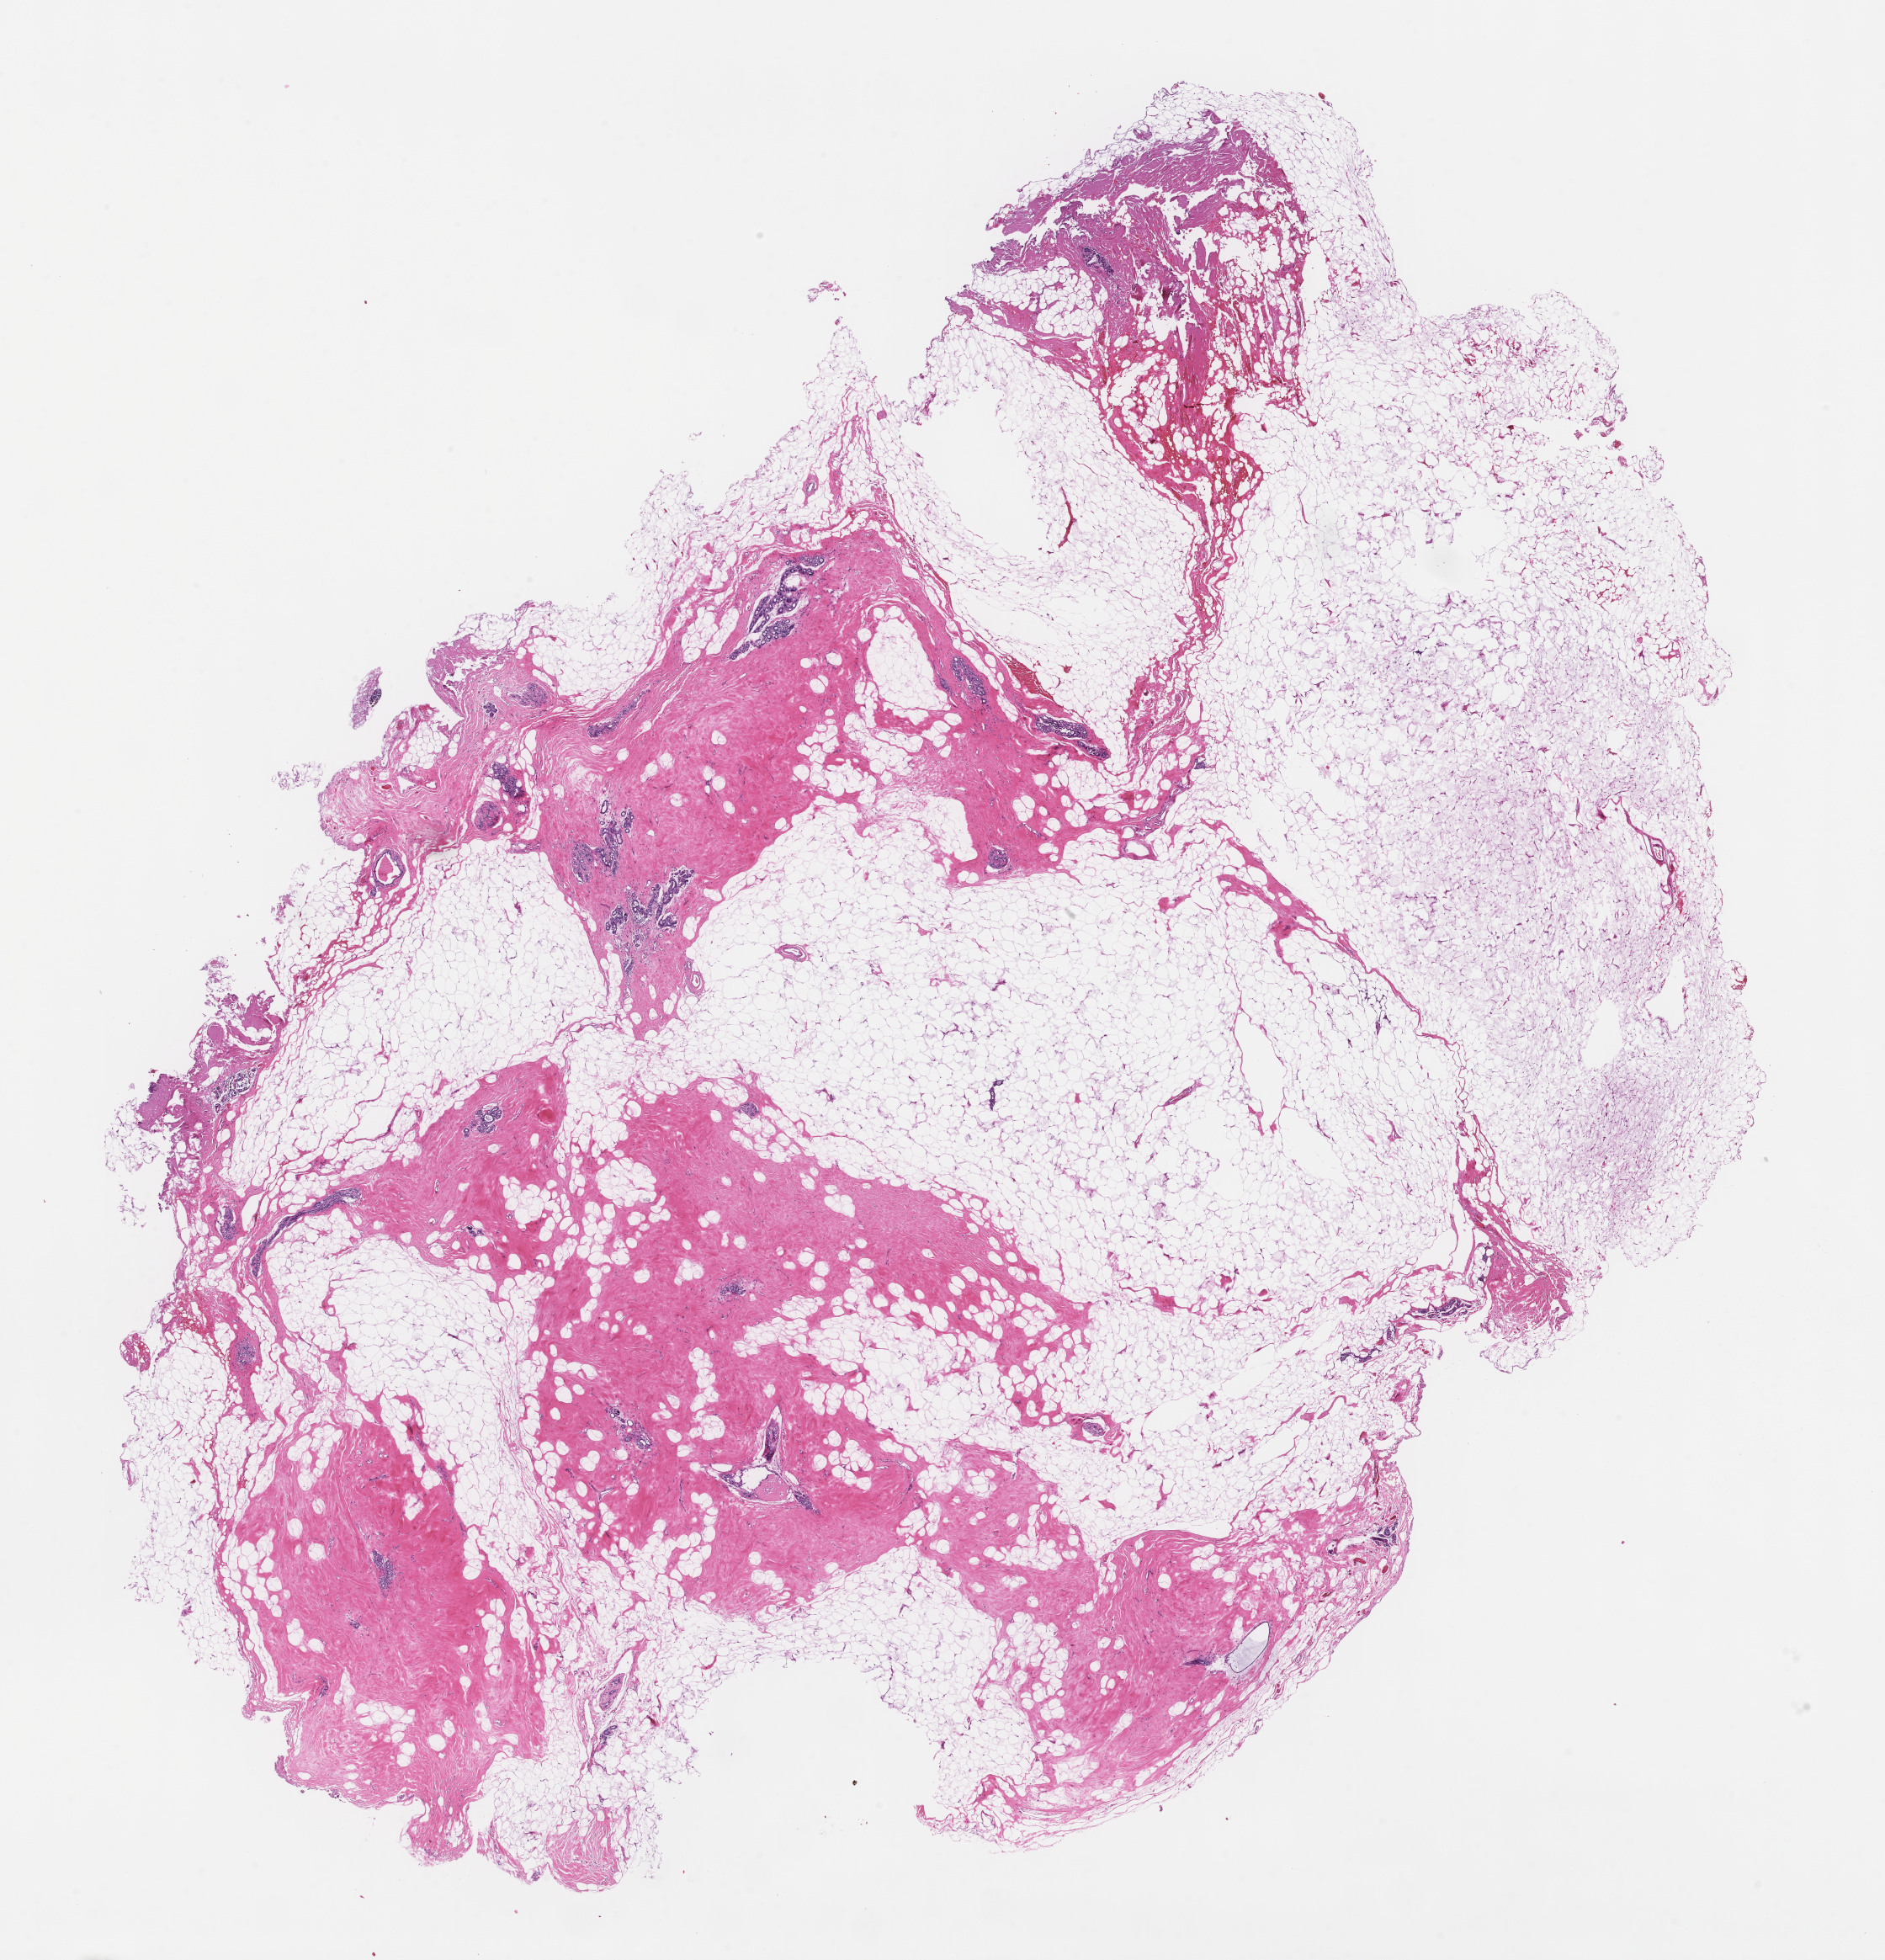
Whole-slide image, haematoxylin and eosin stain — low-resolution overview of the scanned area, about 18.1 x 18.8 mm, formalin-fixed paraffin-embedded section, site: breast, collected post-treatment, no progression. Patient sex: female.
This section: primary tumour tissue. Diagnosis: Invasive Breast Carcinoma.